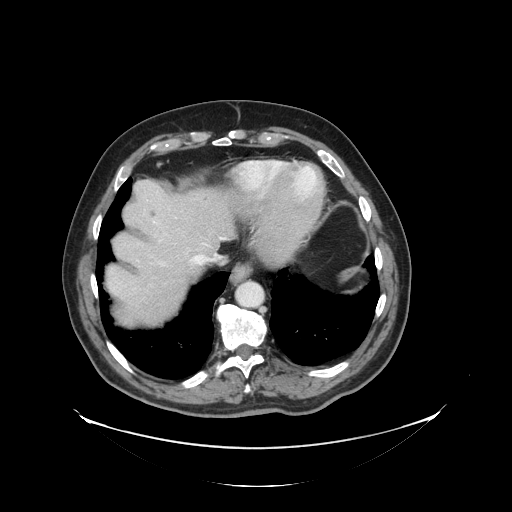
Contrast-enhanced abdominal CT, one axial slice. Slice 116 of 138 in the series (ordered by position). 120 kVp. Intravenous contrast given. Soft-tissue window (W 400 / L 40 HU). 2.5 mm slice thickness. 512 × 512 image matrix, field of view 497 × 497 mm. Male patient, age 77 years. Case-level facts recorded for this patient, not image findings: diagnosis: colorectal cancer liver metastases, imaged before liver resection; multiple liver metastases: no; largest metastasis: 1.5 cm.
Outlined on this slice (expert manual segmentation):
- hepatic veins: bounding box [x1, y1, x2, y2] px = [137, 237, 225, 266]
- liver: [106, 181, 234, 325]
- planned liver remnant (the part of the liver to remain after resection): [106, 181, 235, 290]
- liver metastasis: [151, 212, 157, 218]